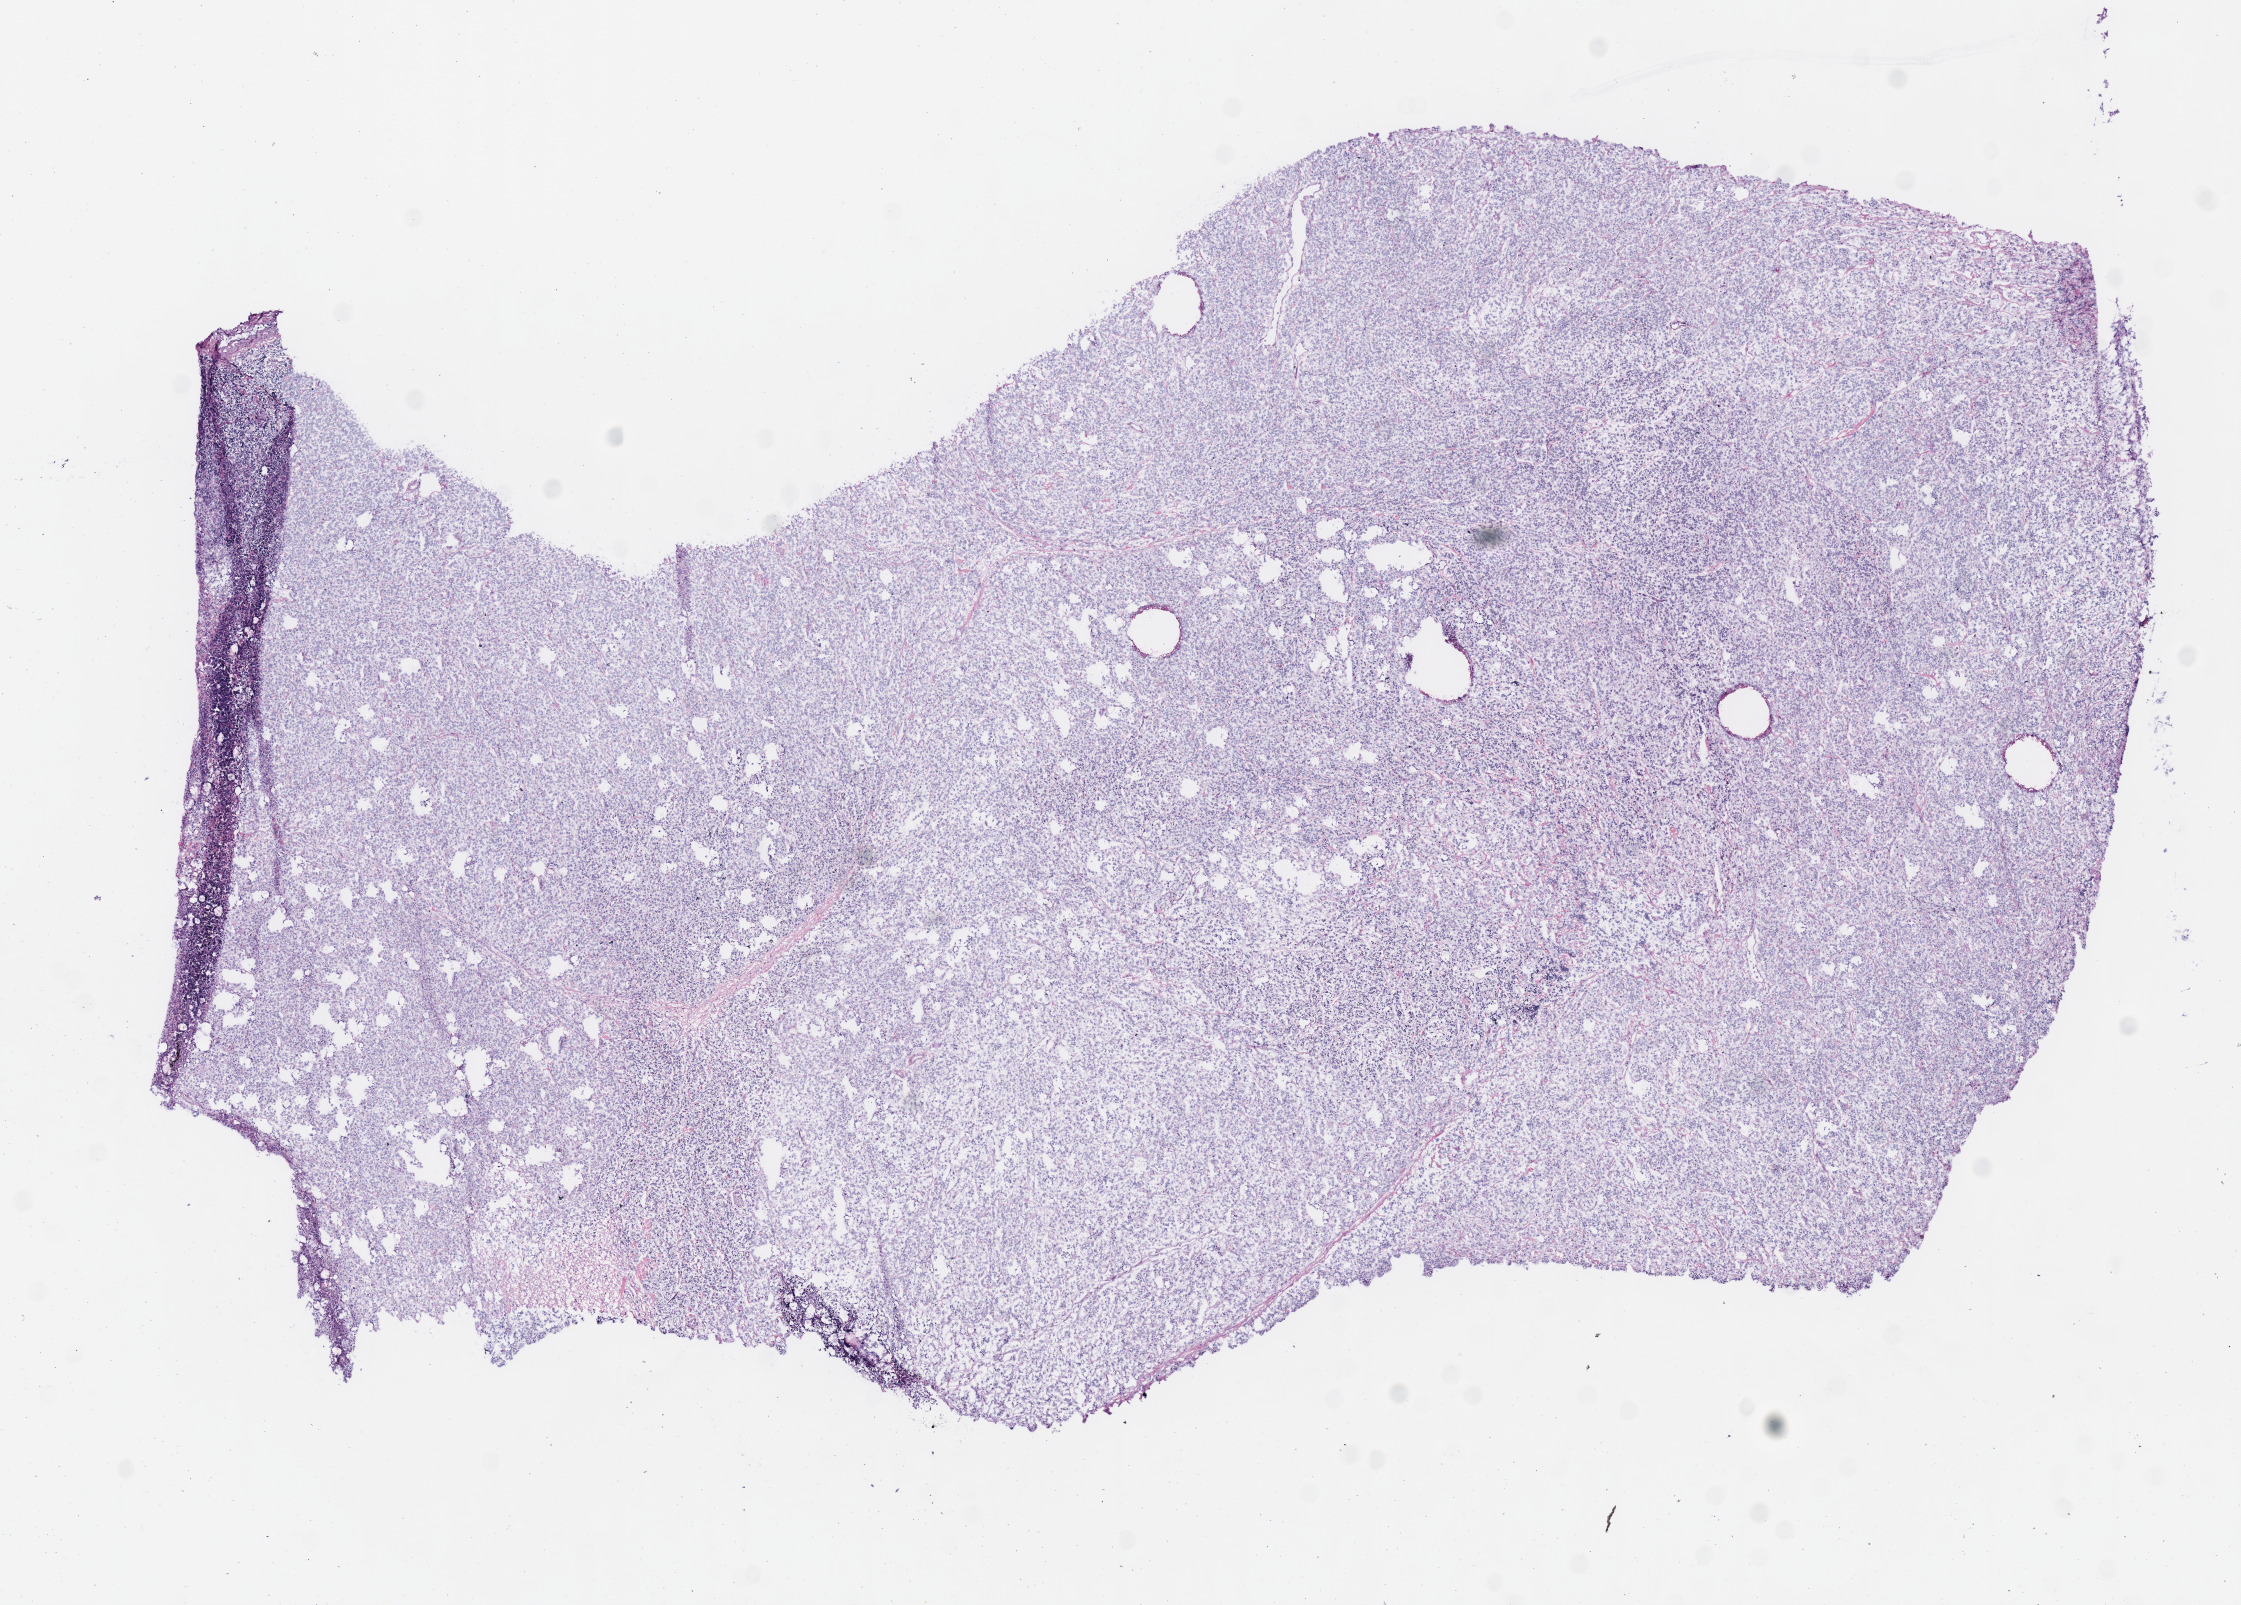
H&E-stained whole-slide image, whole scanned area (about 8.8 x 6.3 mm, slide scanned at 40x) shown as a low-resolution overview, frozen section from the bottom of the tissue portion, primary tumour sample from the lymphoid tissue. Female, age 70 years at initial diagnosis.
* diagnosis: Diffuse large B-cell lymphoma, NOS